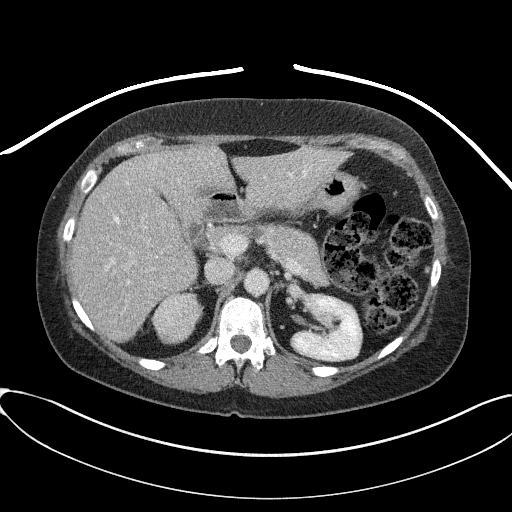
Contrast-enhanced abdominal CT, one axial slice; position 51 of 95 along the scan axis; reconstruction kernel I41f/2; intravenous contrast given; soft-tissue window (W 400 / L 40 HU); 3 mm slice thickness; 512 × 512 image matrix. Female patient, age 46 years. Case-level facts recorded for this patient, not image findings: diagnosis: adrenocortical carcinoma; tumour side: right adrenal; tumour size at pathology: 7.2 cm; Ki-67 index: 50 %; stage (as recorded): 4.
Outlined on this slice (semi-automatically segmented with operator editing):
- mass: bounding box [x1, y1, x2, y2] px = [154, 294, 198, 343]